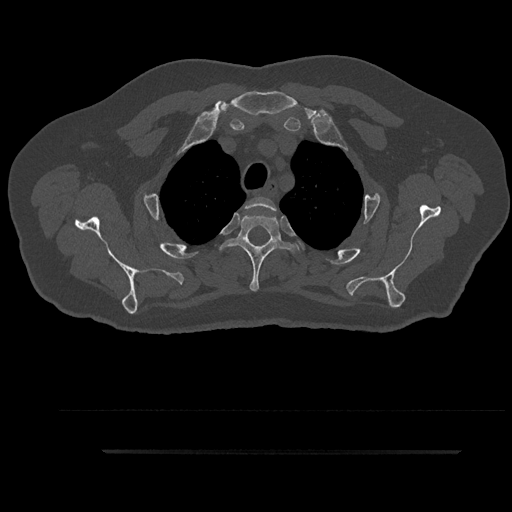
CT including the spine, one axial slice; position 720 of 797 along the scan axis; bone window (W 1800 / L 400 HU); 0.5 mm slice thickness; 512 × 512 image matrix, field of view 432 × 432 mm. Male patient, age 63 years. From the clinical record (not read from this slice): primary cancer: renal.
Structures marked on this image (semi-automatically segmented with operator editing):
- T2 vertebra: bounding box <245,197,276,211> (left, top, right, bottom; pixels)
- T3 vertebra: <221,214,299,292>